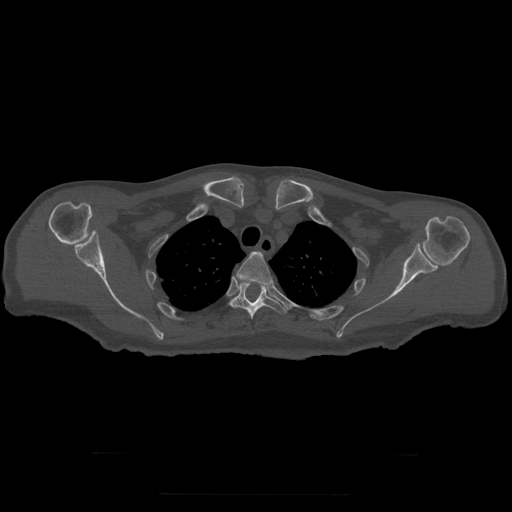
CT including the spine, one axial slice; position 248 of 397 along the scan axis; reconstruction kernel STANDARD; 120 kVp; bone window (W 1800 / L 400 HU); 1.25 mm slice thickness; 512 × 512 image matrix, field of view 510 × 510 mm. Patient age 73 years. From the clinical record (not read from this slice): primary cancer: prostate.
Outlined on this slice (semi-automatically segmented with operator editing):
- T3 vertebra: bounding box <237,252,272,287> (left, top, right, bottom; pixels)
- T4 vertebra: <230,281,287,320>